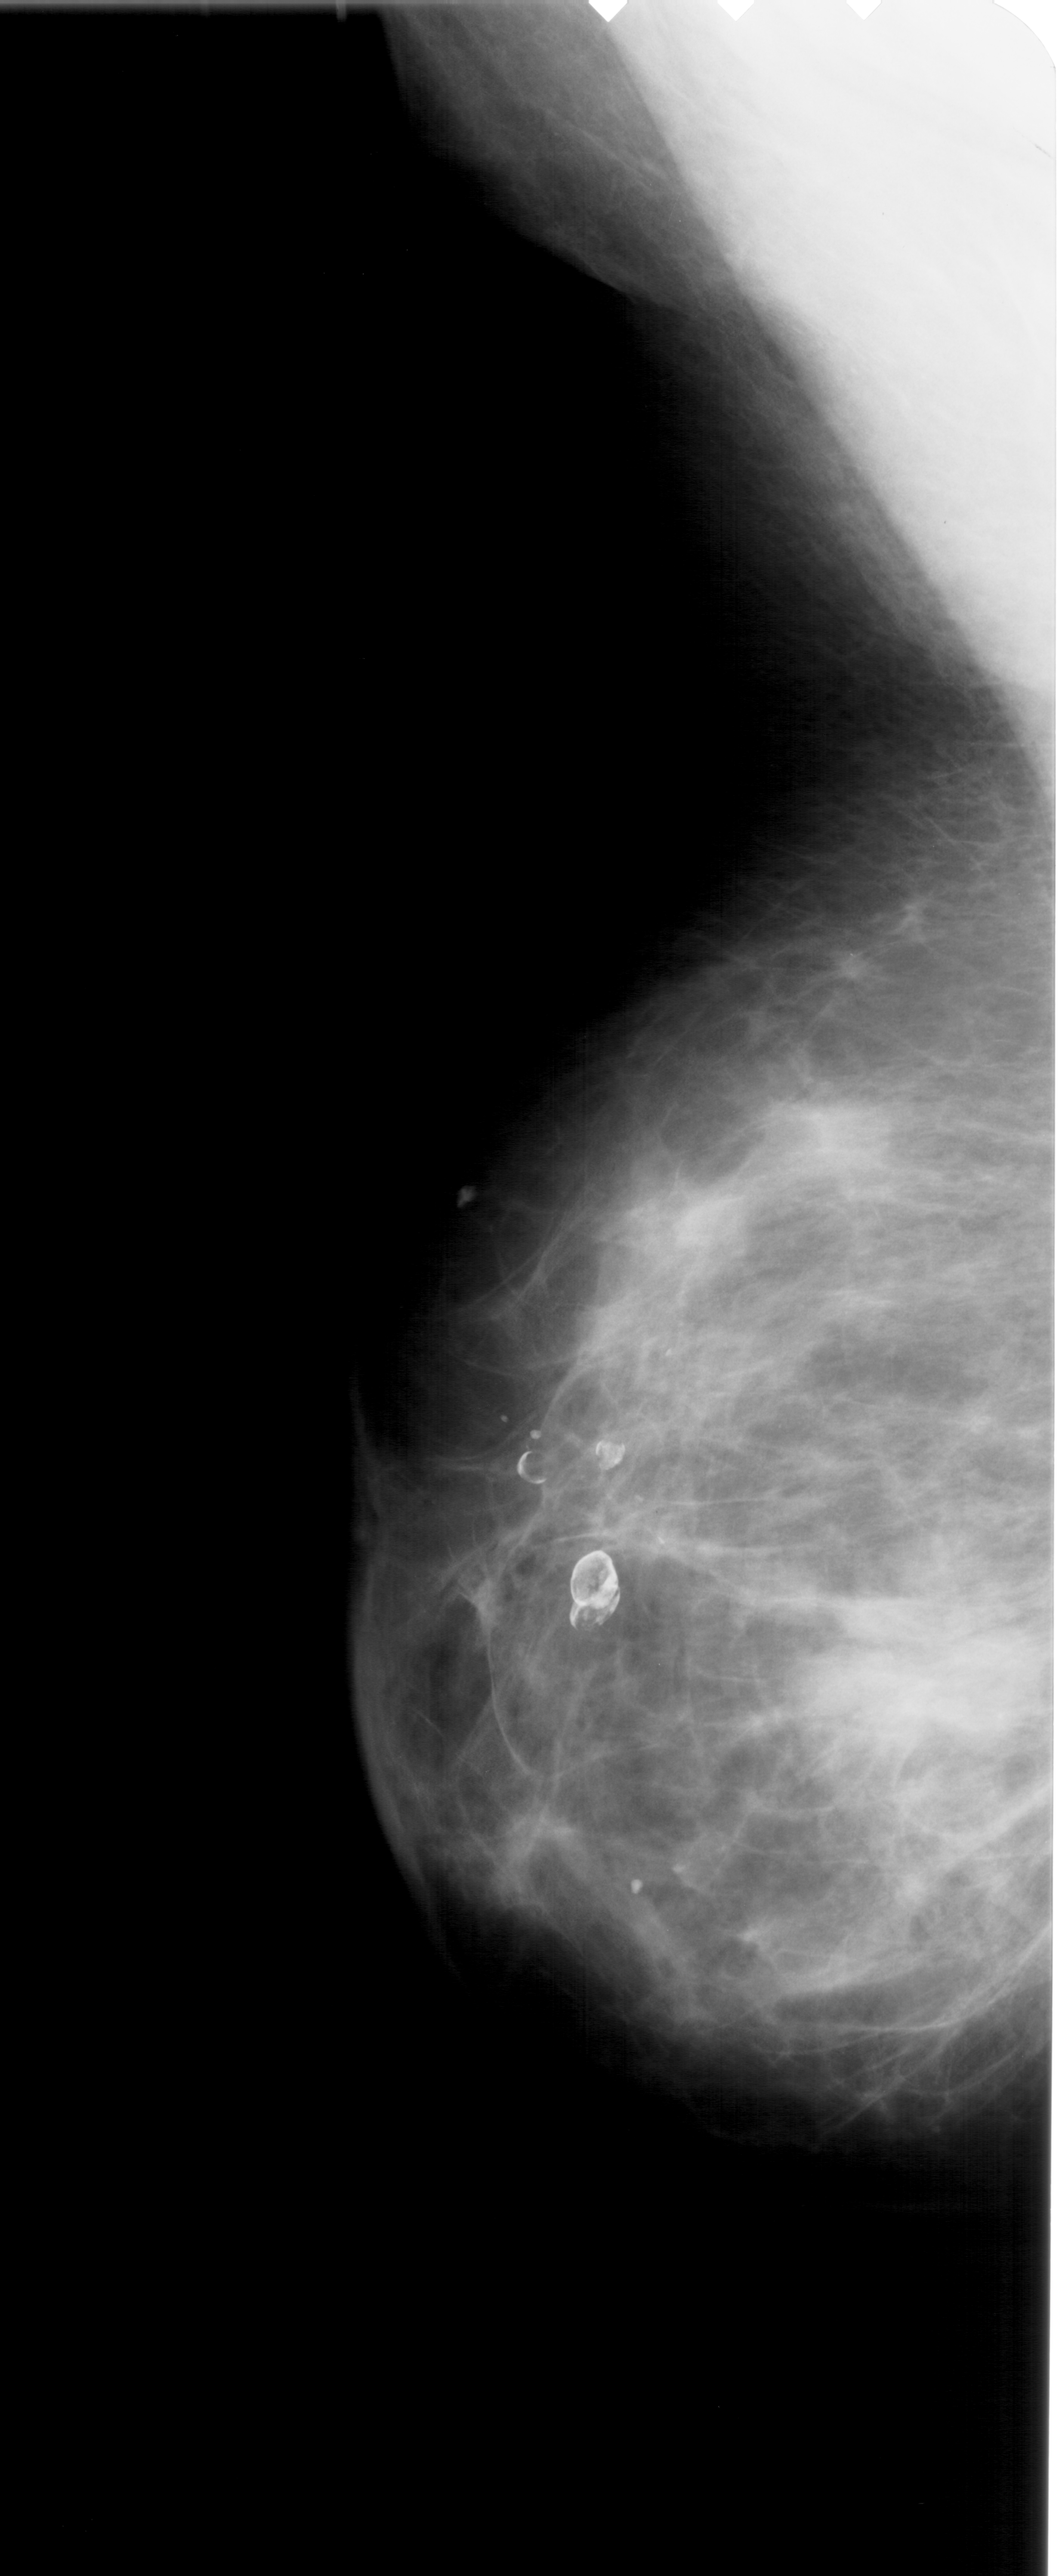
Mammogram (digitized film); left breast; mediolateral oblique (MLO) view; BI-RADS breast density category 2 (scale 1–4).
Marked abnormality: mass, shape irregular, margins ill defined; BI-RADS assessment category 5; pathology (as recorded): malignant.